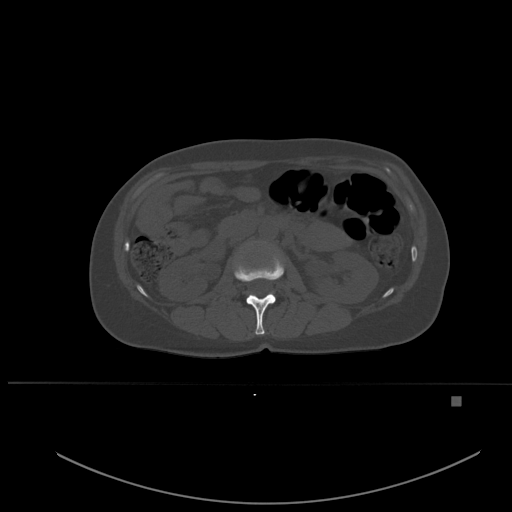
CT including the spine, one axial slice; bone window (W 1800 / L 400 HU); 1.5 mm slice thickness; 512 × 512 image matrix, field of view 443 × 443 mm. Female patient, age 49 years. Case-level facts recorded for this patient, not image findings: primary cancer: breast.
Outlined on this slice (semi-automatic segmentation, software-assisted and operator-edited):
- L1 vertebra: bounding box <234,257,284,335> (left, top, right, bottom; pixels)